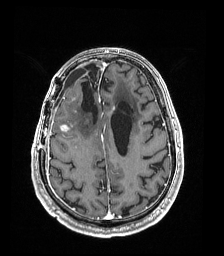
Brain MRI from a brain-tumour surgery series, one axial slice; position 58 of 192 along the scan axis; T1-weighted post-contrast; 1 mm slice thickness; 224 × 256 image matrix, field of view 224 × 256 mm. Case-level facts recorded for this patient, not image findings: histopathology: Astrocytoma; WHO grade: 4; IDH mutation: yes.
Outlined on this slice (expert manual segmentation):
- previous resection cavity: box from (x=81, y=68) to (x=98, y=122) px